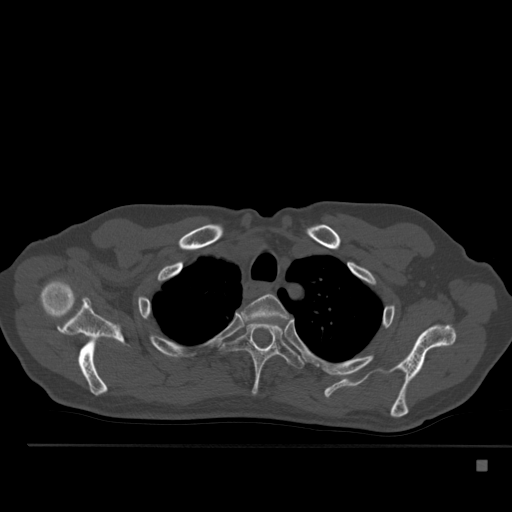
CT including the spine, one axial slice; position 401 of 517 along the scan axis; 120 kVp; bone window (W 1800 / L 400 HU); 512 × 512 image matrix, field of view 408 × 408 mm. Patient: male, 70 years. Case-level facts recorded for this patient, not image findings: primary cancer: renal; vertebrae with lytic lesions (as recorded): T4, T6, T10, T12, L3, L4, L5.
Outlined on this slice (semi-automatic segmentation, software-assisted and operator-edited):
- T2 vertebra: bounding box (x1, y1, x2, y2) in pixels: (242, 294, 290, 321)
- T3 vertebra: (220, 323, 304, 396)